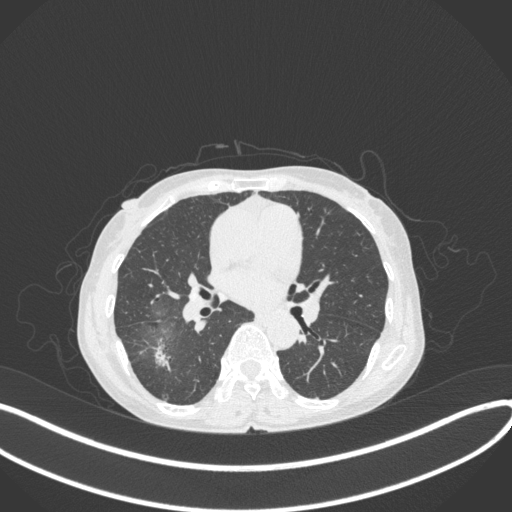
Chest CT, one axial slice; slice 205 of 379 in the series (ordered by position); reconstruction kernel B31f; 120 kVp; lung window (W 1500 / L -600 HU); 1 mm slice thickness; 512 × 512 image matrix, field of view 400 × 400 mm. Female patient, age 69 years. Case-level facts recorded for this patient, not image findings: clinical TNM (as recorded): T1b N0 M0; histopathological grade: G2-3.
Structures marked on this image (bounding box drawn by a radiologist):
- lung tumour (recorded histology: adenocarcinoma): bounding box <152,336,177,371> (left, top, right, bottom; pixels)